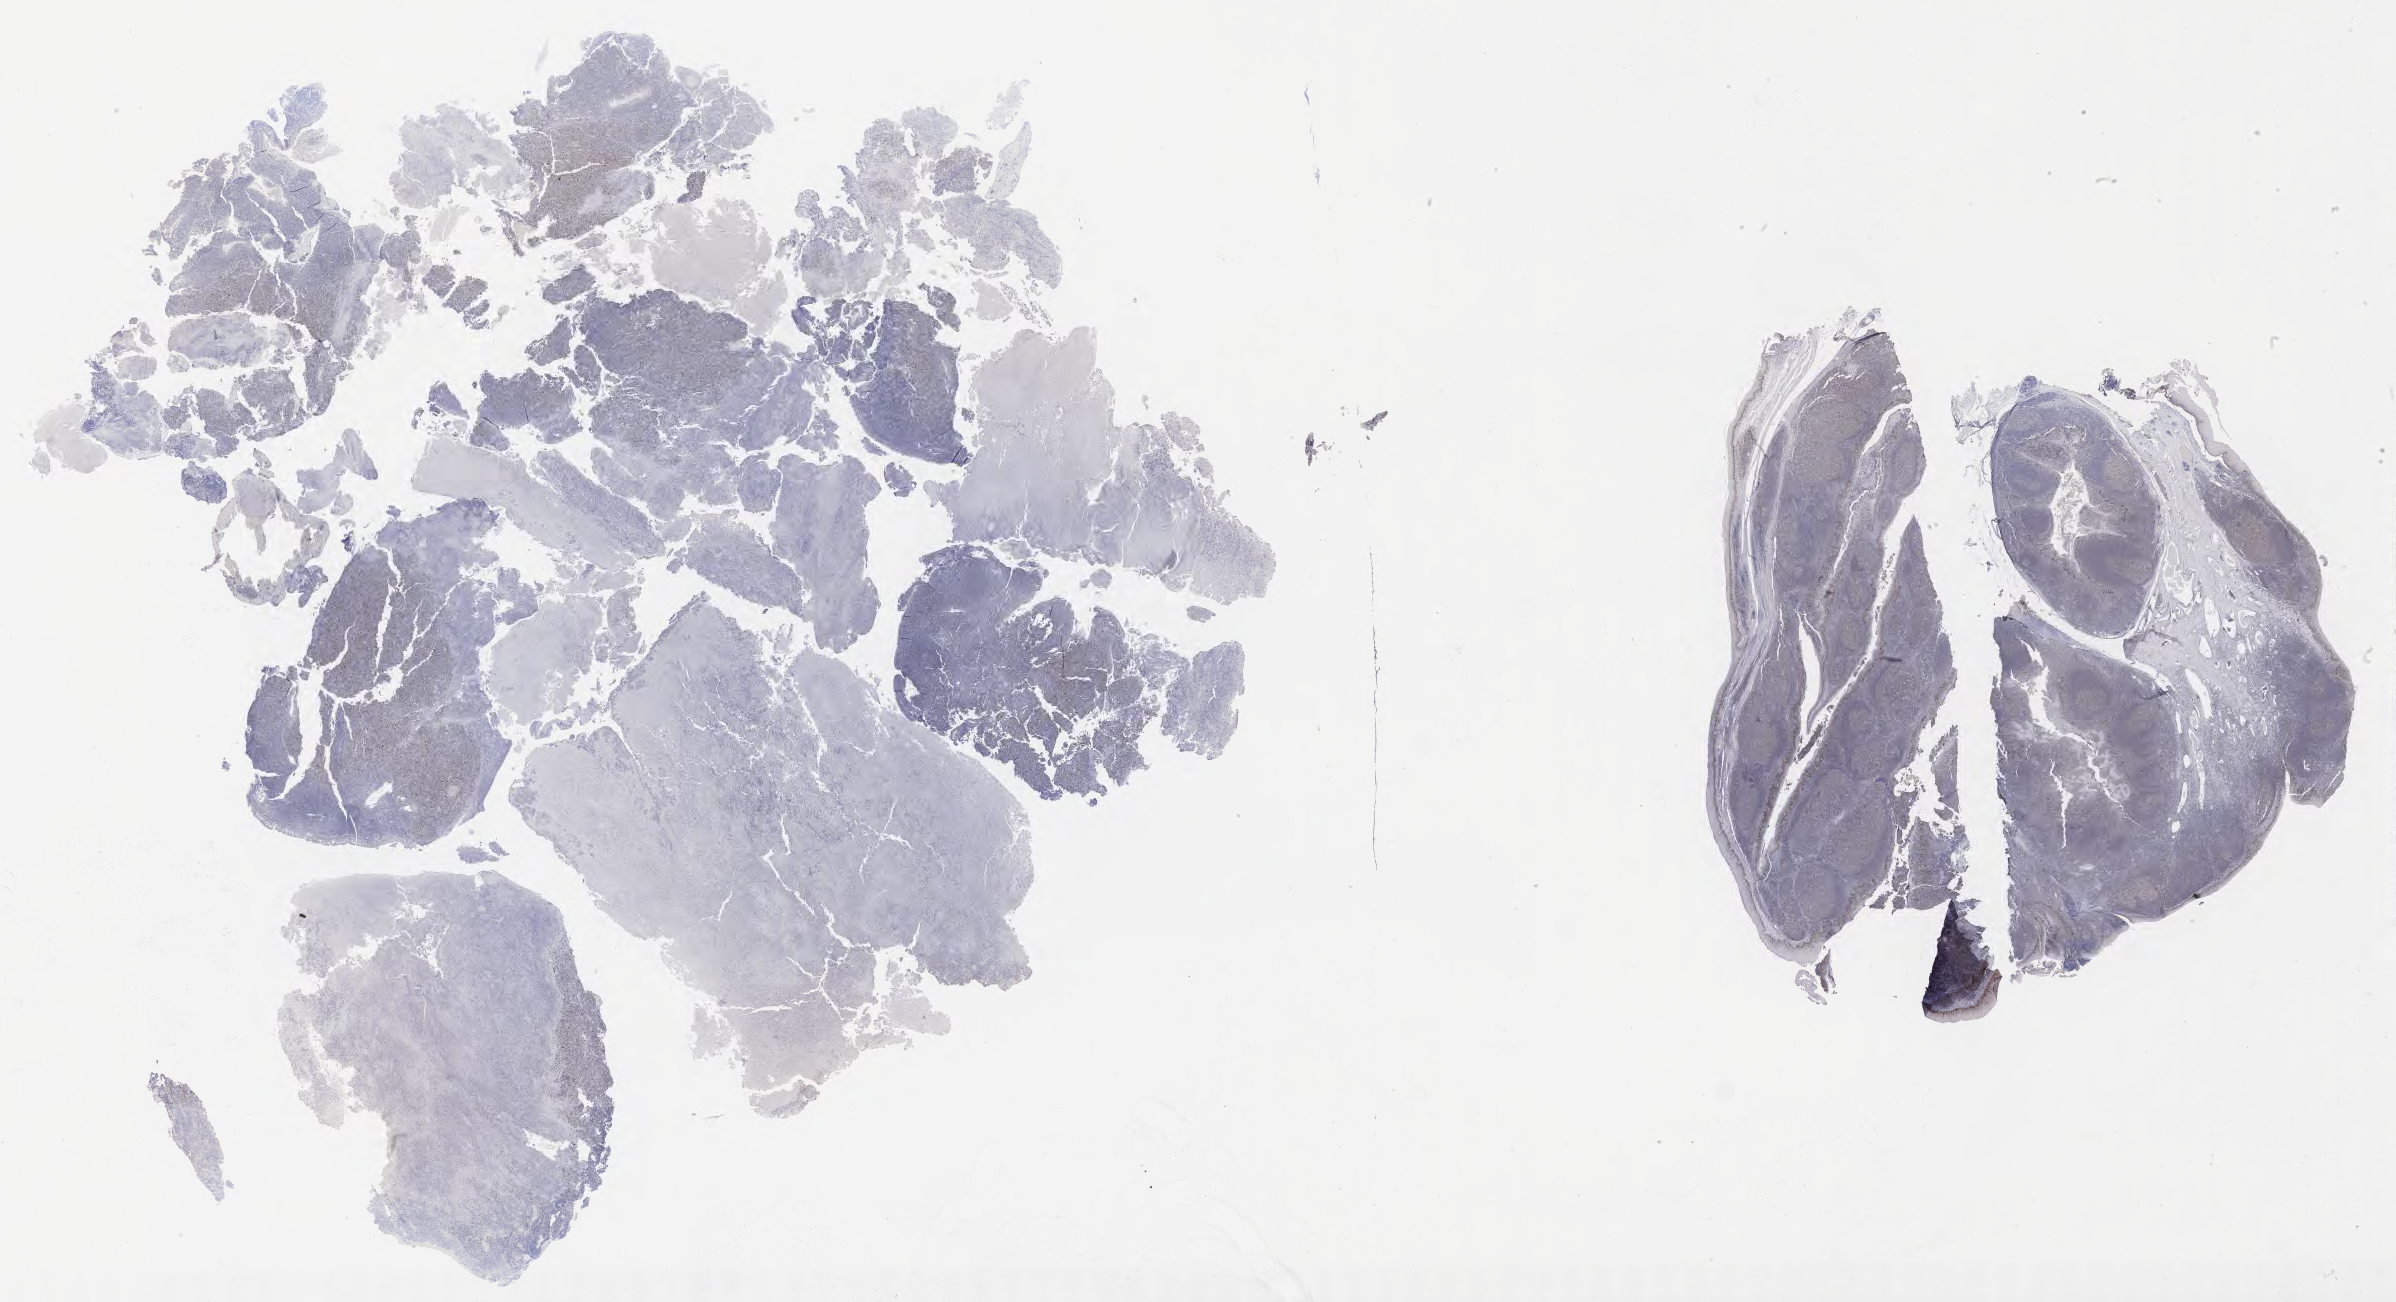
IHC for p53, whole-slide image — whole scanned area (about 38.7 x 21.1 mm) shown as a low-resolution overview. Specimen: tumor tissue. Patient male; 47 years old.
Histologic diagnosis: Diffuse large B-cell lymphoma, NOS.